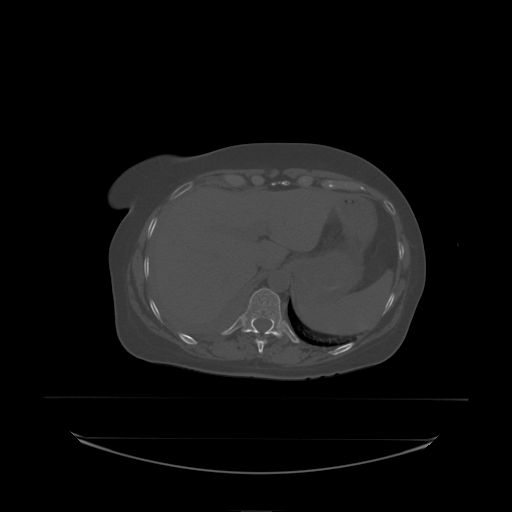
CT including the spine, one axial slice; position 107 of 242 along the scan axis; bone window (W 1800 / L 400 HU); 2.5 mm slice thickness; 512 × 512 image matrix, field of view 500 × 500 mm. Patient: female, 53 years. From the clinical record (not read from this slice): primary cancer: lung.
Structures marked on this image (semi-automatically segmented with operator editing):
- T11 vertebra: box from (x=242, y=289) to (x=283, y=336) px